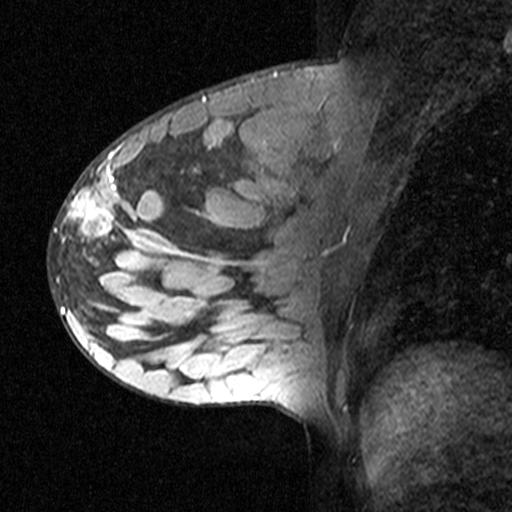
Breast MRI (dynamic contrast-enhanced), one sagittal slice. Slice 19 of 44 in the series (ordered by position). Dynamic contrast-enhanced study with each time point stored as its own series, time point 2 of 3 at this slice position (early post-contrast, ordered by acquisition time). 1.5 T. TE 4.5 ms, TR 11 ms. 512 × 512 image matrix, field of view 200 × 200 mm. Female patient, age 27 years. Case-level facts recorded for this patient, not image findings: setting: breast cancer imaged before/during neoadjuvant chemotherapy; receptor status: HR-positive, HER2-negative.
Outlined on this slice (semi-automatic segmentation, software-assisted and operator-edited):
- analysis volume of interest (the breast-tissue region the enhancement analysis was run in; not a lesion): bounding box [x1, y1, x2, y2] px = [49, 162, 163, 271]
- tumour enhancement mask (voxels above the 90 % enhancement threshold inside the analysis volume of interest): [54, 162, 123, 242]